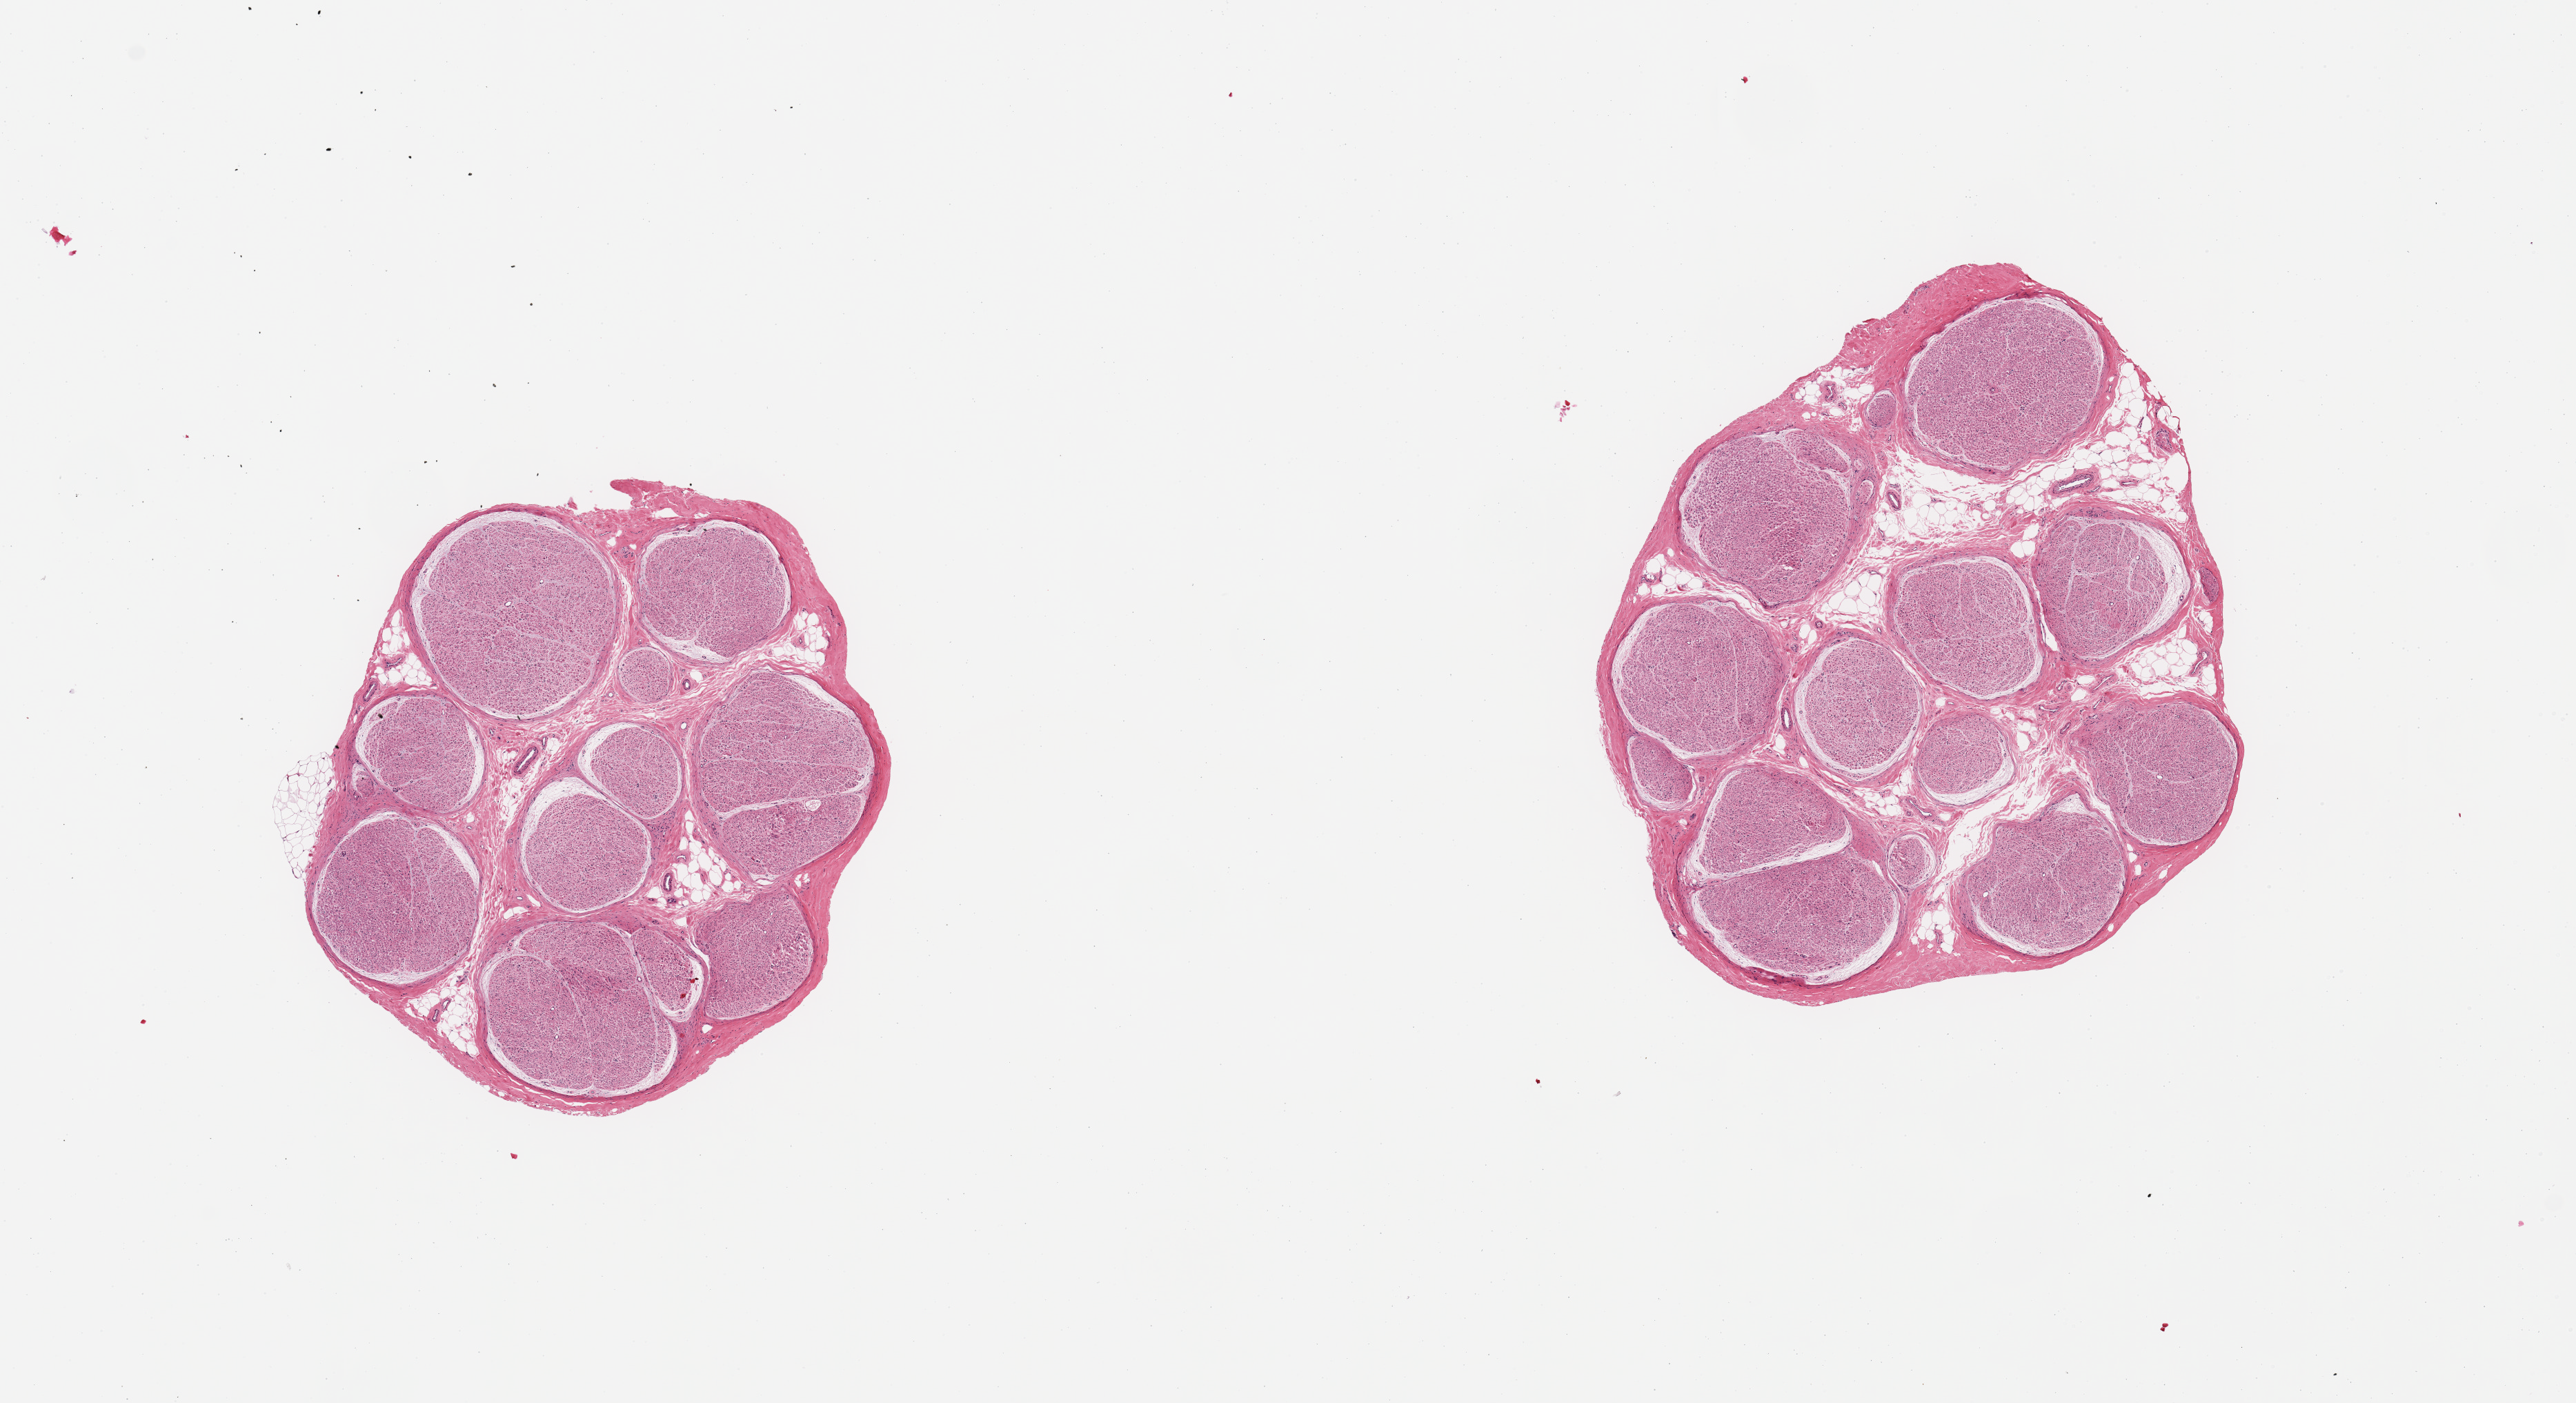
Haematoxylin and eosin whole-slide image, whole scanned area (about 14.8 x 8.0 mm, from a 20x scan) shown as a low-resolution overview; PAXgene-fixed paraffin-embedded (PFPE) section; section of tibial nerve (target tissue); donor tissue sample. Donor: male.
Reviewer comment on this tissue sample: 2 pieces, no adherent fat.